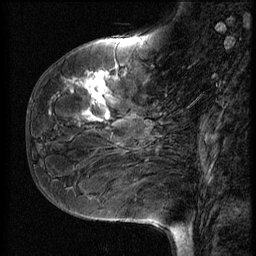
Breast MRI (dynamic contrast-enhanced), one sagittal slice. Slice 22 of 56 in the series (ordered by position). 3 images stored at this slice position (order not interpretable as contrast timing). 1.5 T. TE 4.2 ms, TR 9 ms. 256 × 256 image matrix, field of view 180 × 180 mm. Patient: female, 51 years. From the clinical record (not read from this slice): setting: breast cancer imaged before/during neoadjuvant chemotherapy; receptor status: HR-positive, HER2-negative.
Annotated regions visible in this slice (semi-automatic segmentation, software-assisted and operator-edited):
- analysis volume of interest (the breast-tissue region the enhancement analysis was run in; not a lesion): bounding box [x1, y1, x2, y2] px = [41, 58, 167, 161]
- tumour enhancement mask (voxels above the 140 % enhancement threshold inside the analysis volume of interest): [68, 71, 116, 123]